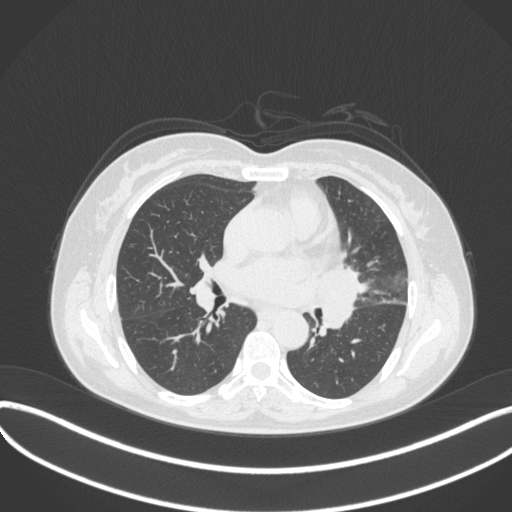
Chest CT, one axial slice. Slice 183 of 373 in the series (ordered by position). Lung window (W 1500 / L -600 HU). 512 × 512 image matrix. Patient: female, 54 years. From the clinical record (not read from this slice): clinical TNM (as recorded): T2a N1 M0; histopathological grade: G3.
Annotated regions visible in this slice (bounding box drawn by a radiologist):
- lung tumour (recorded histology: small cell carcinoma): box from (x=314, y=261) to (x=376, y=335) px